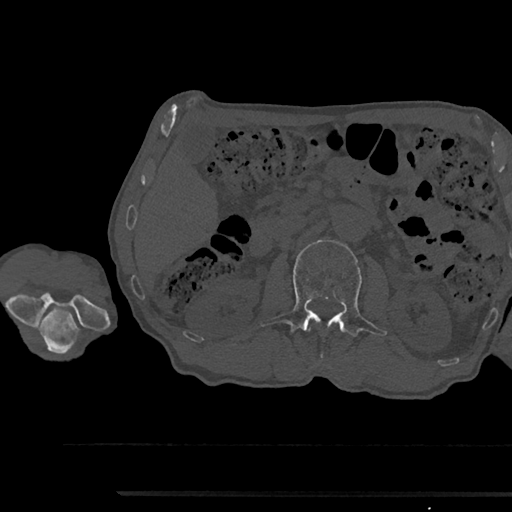
CT including the spine, one axial slice. Slice 575 of 797 in the series (ordered by position). Bone window (W 1800 / L 400 HU). 0.5 mm slice thickness. 512 × 512 image matrix. Male patient, age 79 years. Case-level facts recorded for this patient, not image findings: primary cancer: prostate.
Structures marked on this image (semi-automatic segmentation, software-assisted and operator-edited):
- L2 vertebra: bounding box (x1, y1, x2, y2) in pixels: (260, 240, 387, 363)